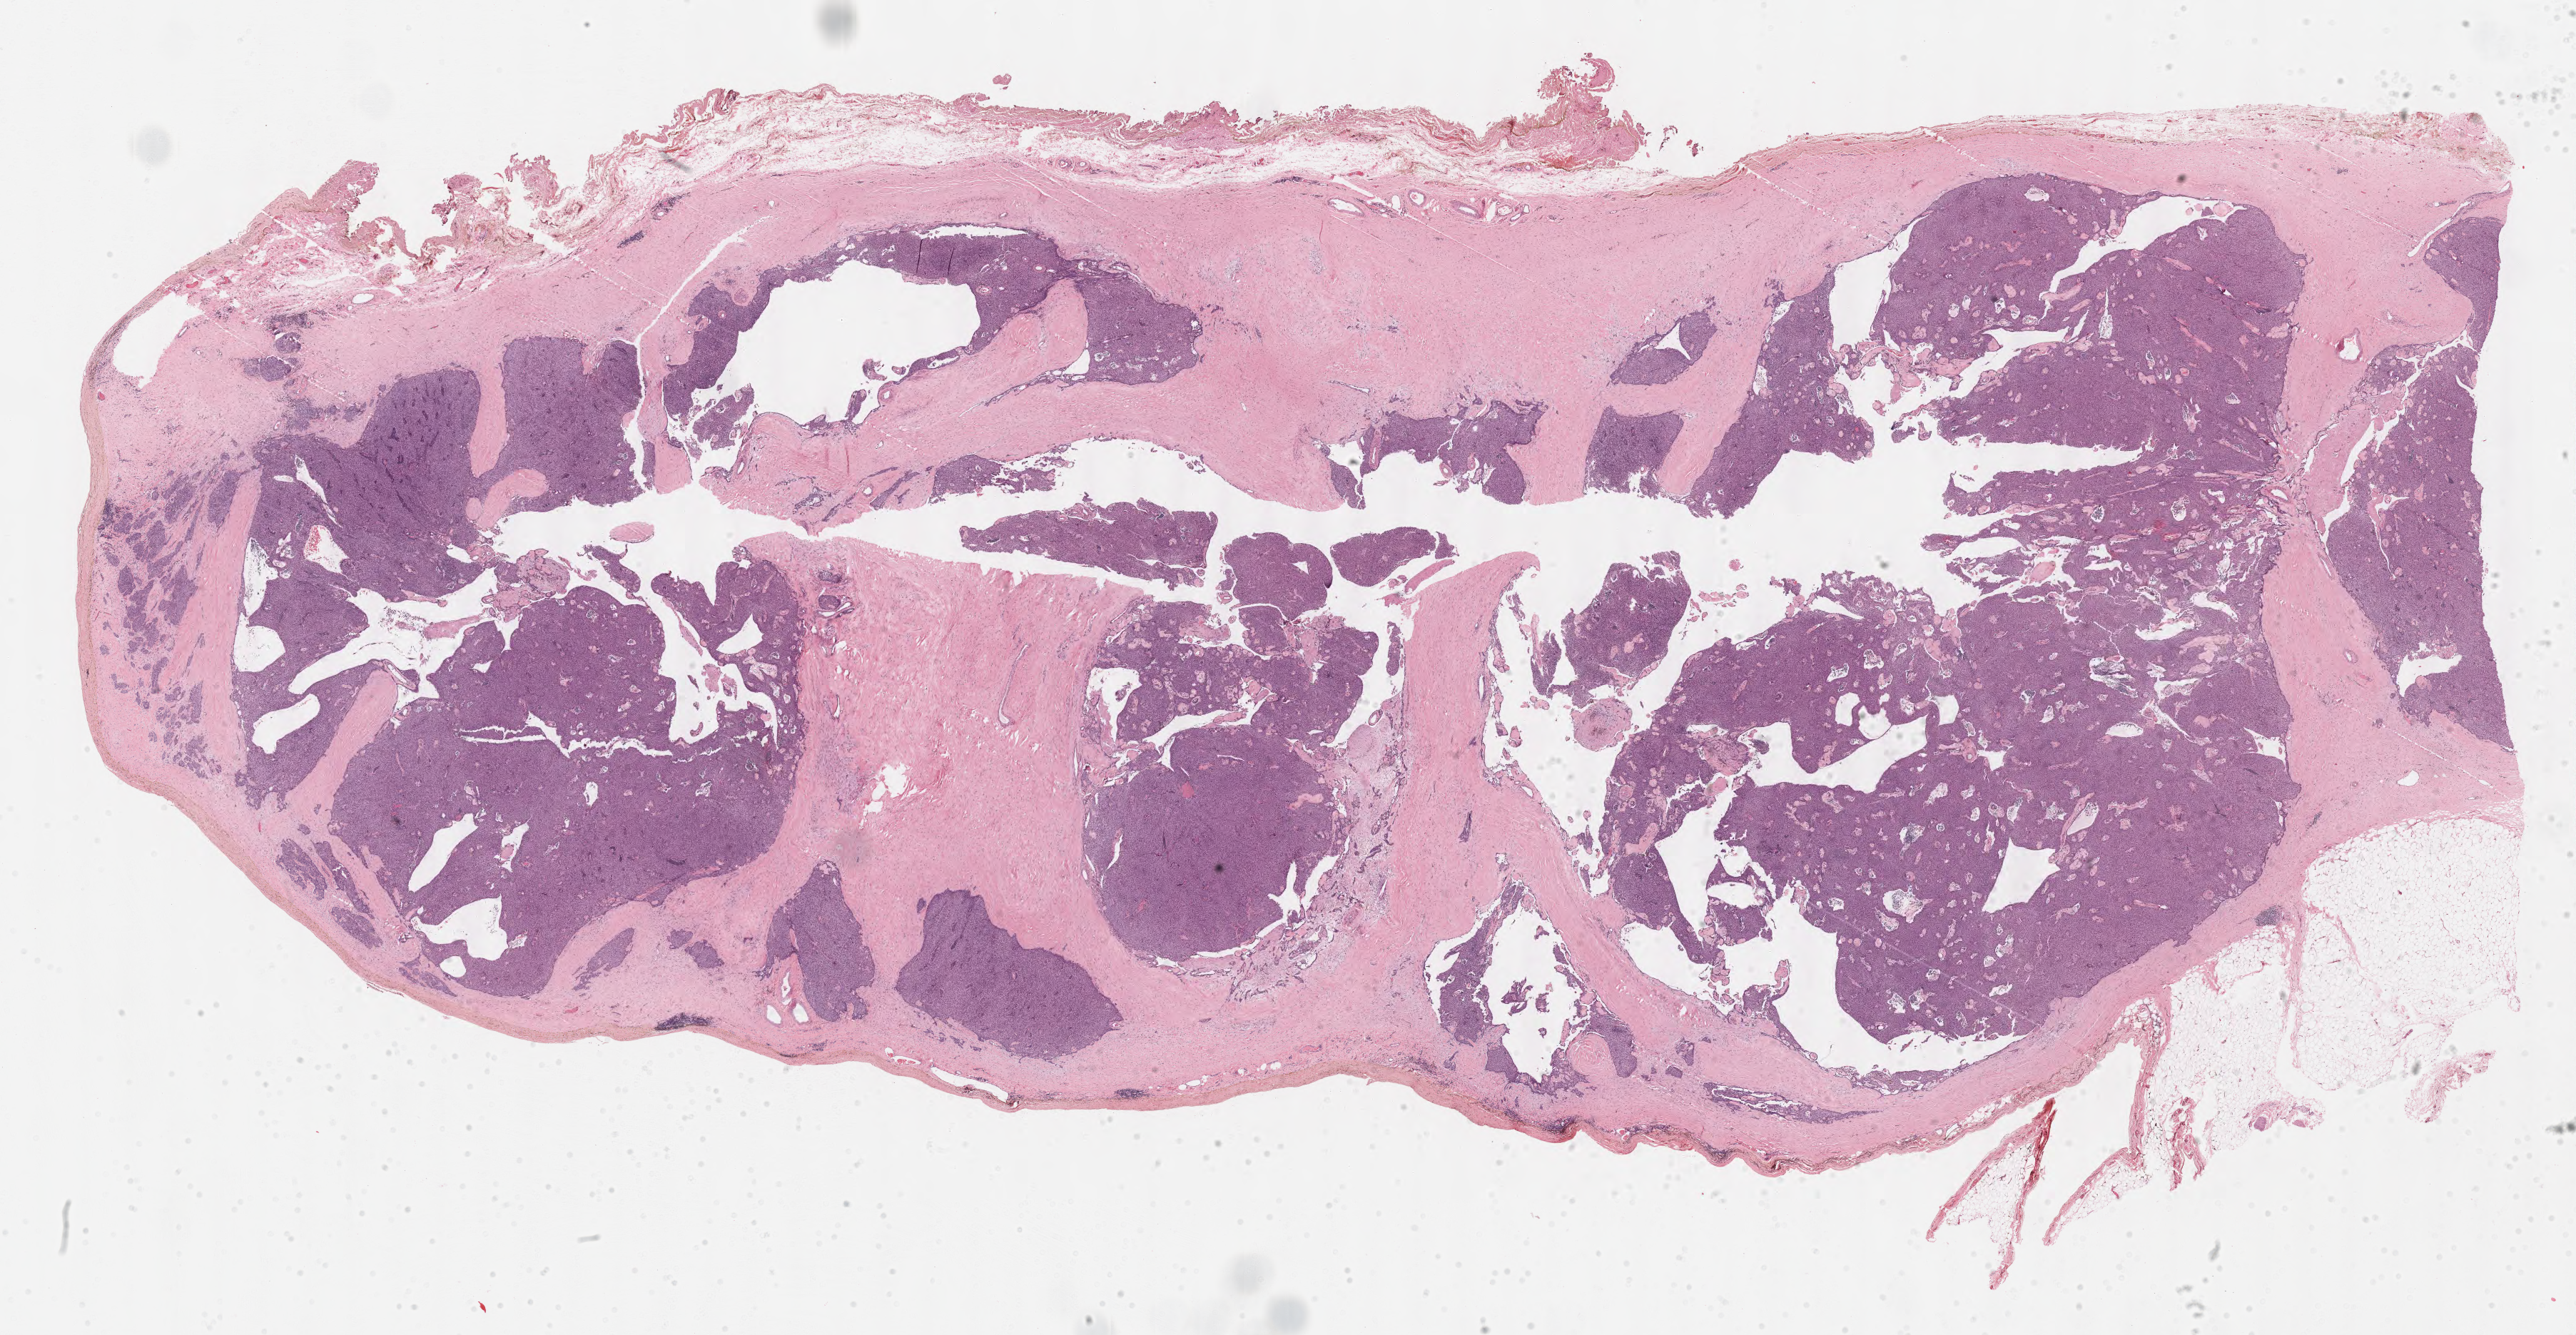
Whole-slide histology image, H&E, whole scanned area (about 28.5 x 14.8 mm, from a 40x scan) shown as a low-resolution overview. FFPE section. Thymus, primary tumour sample. Female patient; age at initial diagnosis 61 years.
Diagnosis: Thymoma, type B3, malignant.